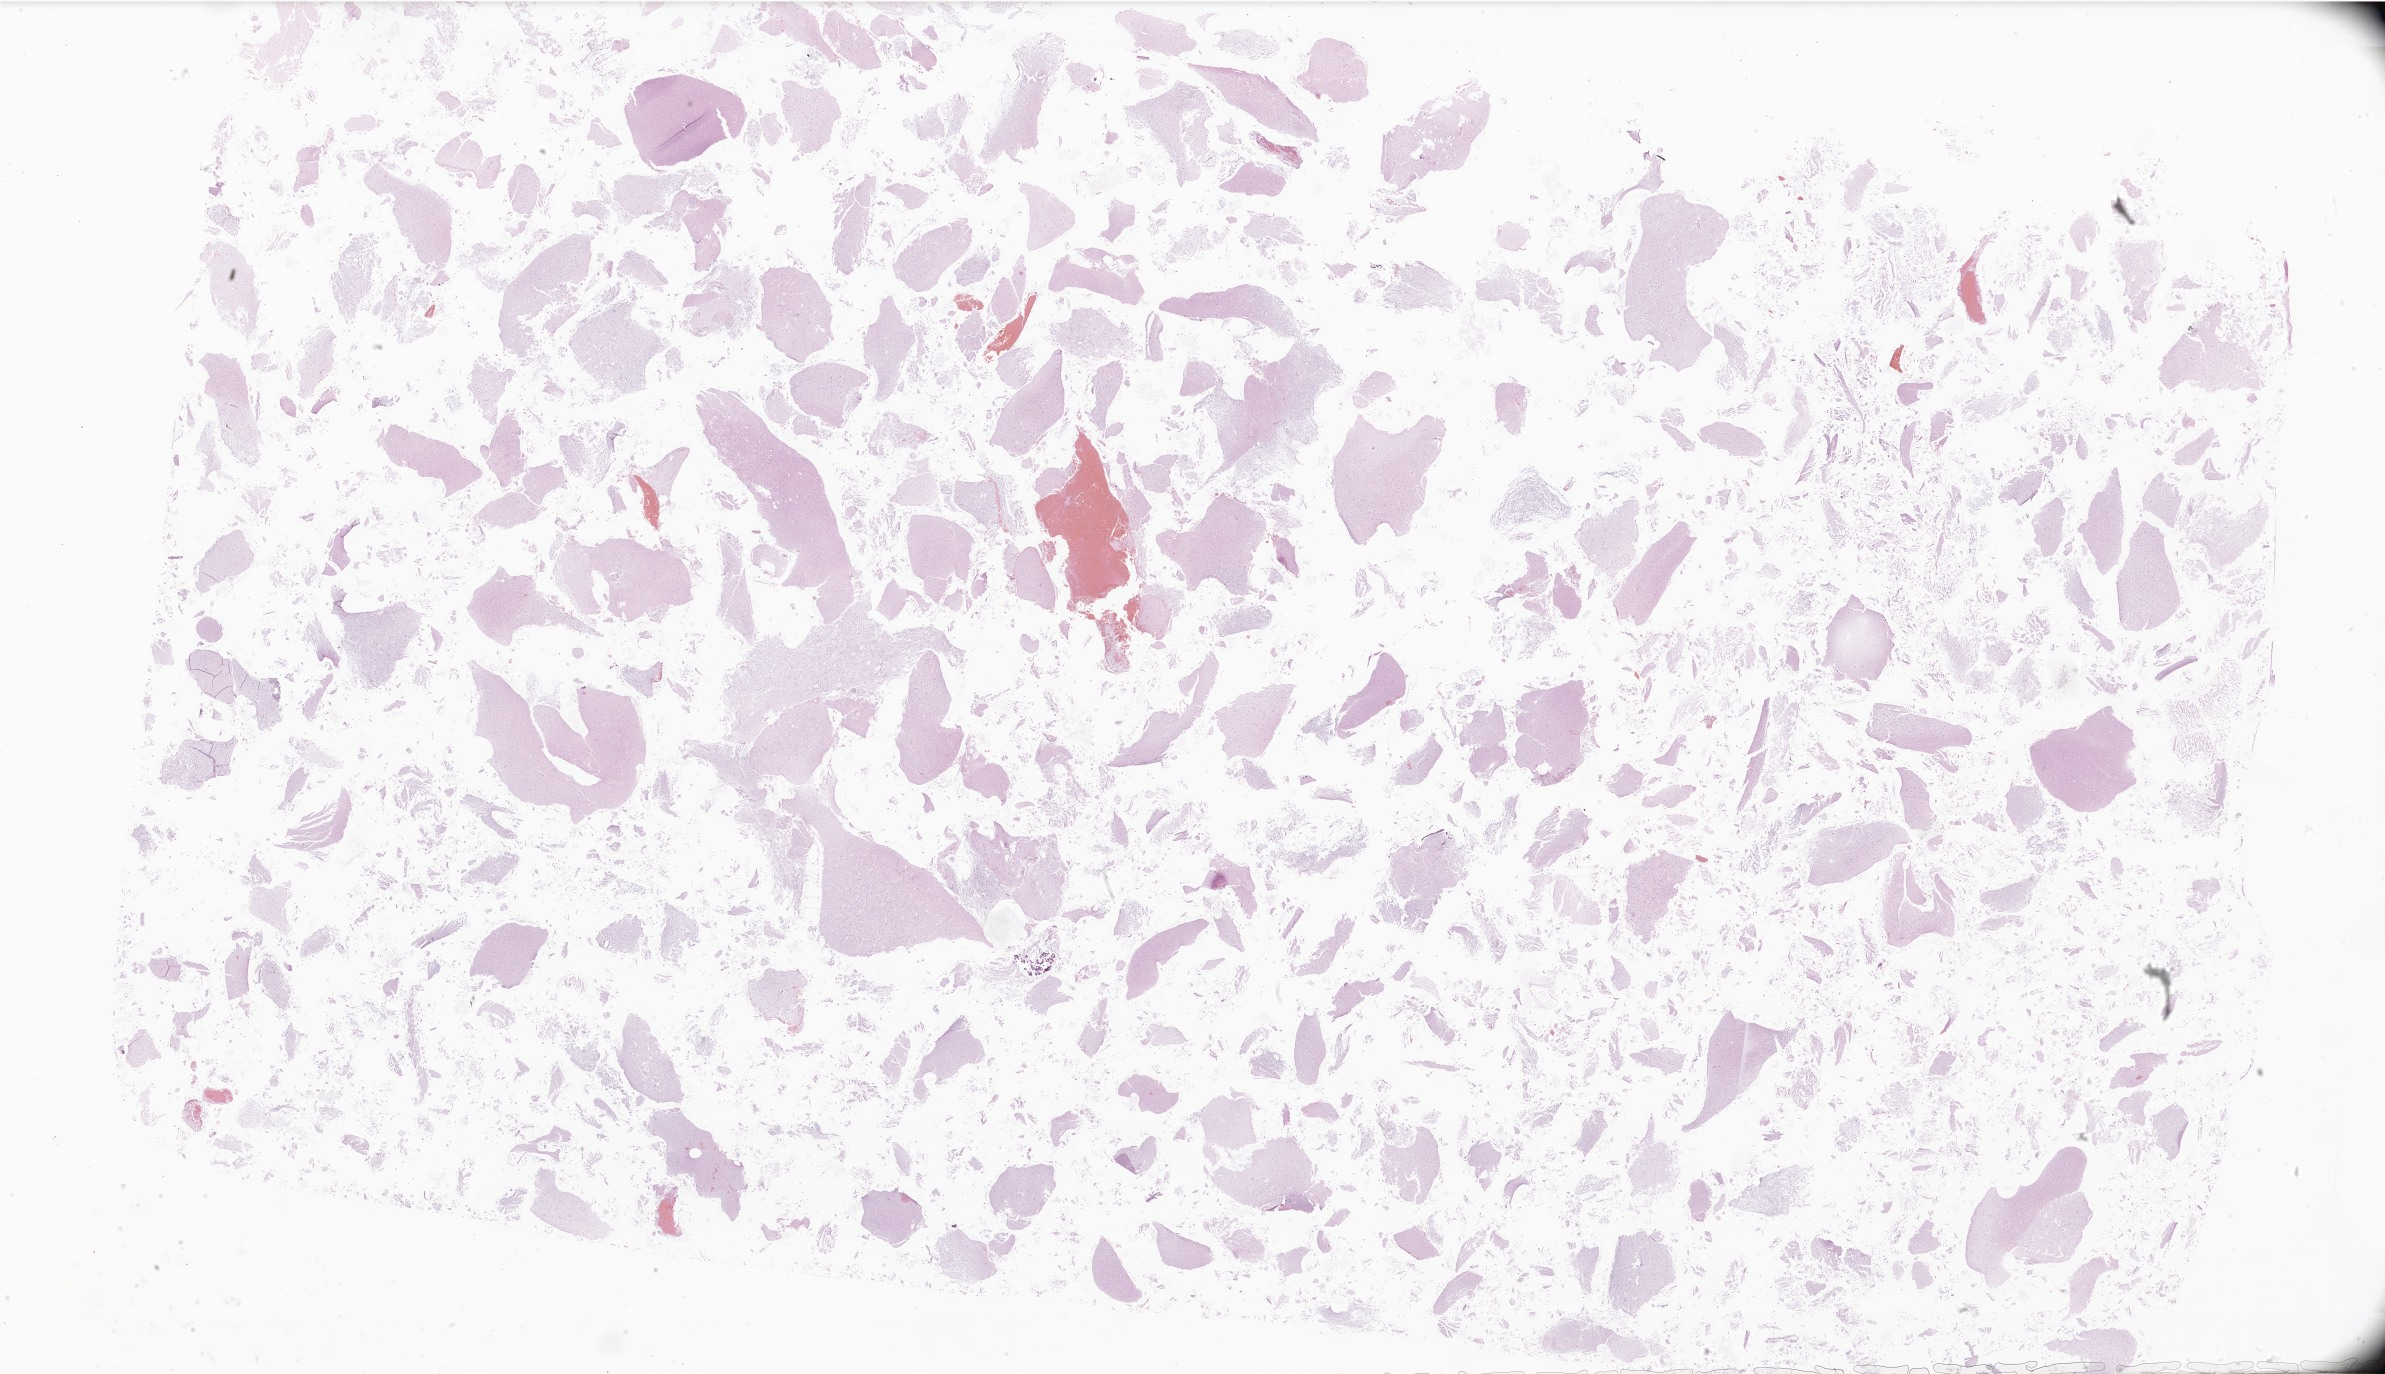
H&E whole-slide image of tumor tissue from the brain, a low-resolution overview of the entire scanned area, about 40.2 x 23.2 mm, formalin-fixed, paraffin-embedded (FFPE) tissue. Patient male; age 89 months.
* diagnosis (ICD-O-3 morphology term): Dysembryoplastic neuroepithelial tumor